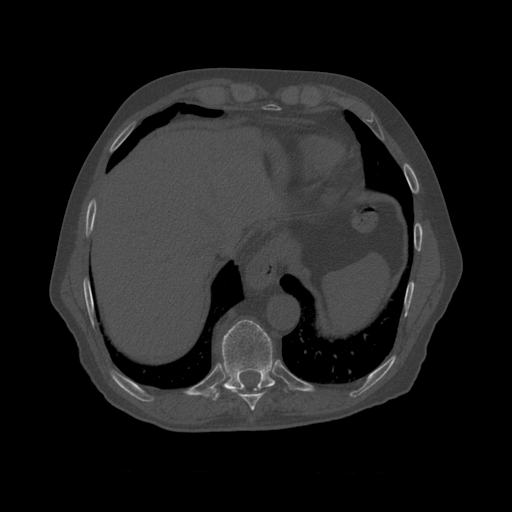
CT including the spine, one axial slice. Slice 434 of 450 in the series (ordered by position). Bone window (W 1800 / L 400 HU). 1.25 mm slice thickness. 512 × 512 image matrix, field of view 405 × 405 mm. Patient age 75 years. Case-level facts recorded for this patient, not image findings: primary cancer: prostate.
Annotated regions visible in this slice (semi-automatically segmented with operator editing):
- T8 vertebra: bounding box <230,370,265,410> (left, top, right, bottom; pixels)
- T9 vertebra: <215,320,276,394>